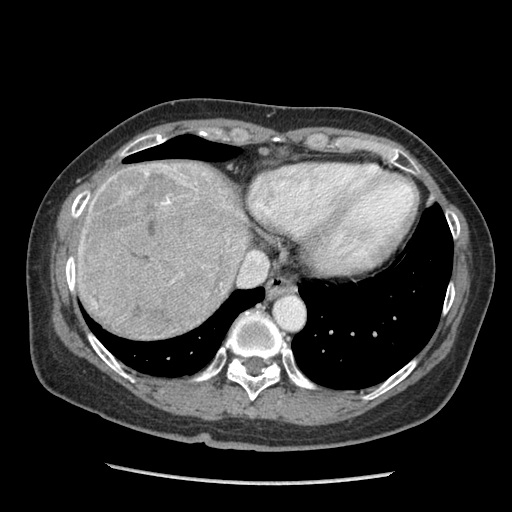
Contrast-enhanced abdominal CT (liver protocol), one axial slice; position 81 of 105 along the scan axis; reconstruction kernel STANDARD; soft-tissue window (W 400 / L 40 HU); 2.5 mm slice thickness; 512 × 512 image matrix, field of view 340 × 340 mm. Case-level facts recorded for this patient, not image findings: diagnosis: hepatocellular carcinoma (patient treated with transarterial chemoembolisation; whether this scan precedes or follows treatment is not stated here); TNM stage (as recorded): Stage-I; Child-Pugh class: A; tumour size: 11.1 cm.
Structures marked on this image (semi-automatic segmentation, software-assisted and operator-edited):
- liver parenchyma outside the tumour (the mass and vessels are separate outlines, so this box may not span the whole liver): bounding box <74,162,250,326> (left, top, right, bottom; pixels)
- mass: <78,164,233,340>